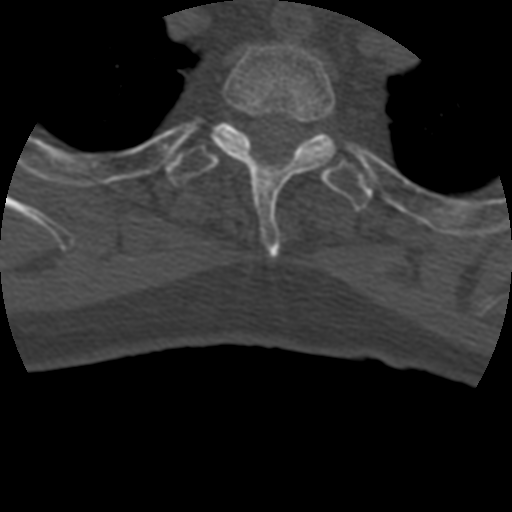
CT including the spine, one axial slice. Position 362 of 399 along the scan axis. Reconstruction kernel STANDARD. 120 kVp. Bone window (W 1800 / L 400 HU). 1.25 mm slice thickness. 512 × 512 image matrix, field of view 160 × 160 mm. Patient age 69 years. Case-level facts recorded for this patient, not image findings: primary cancer: prostate.
Outlined on this slice (semi-automatic segmentation, software-assisted and operator-edited):
- T2 vertebra: bounding box (x1, y1, x2, y2) in pixels: (213, 42, 336, 255)
- T3 vertebra: (168, 121, 374, 211)